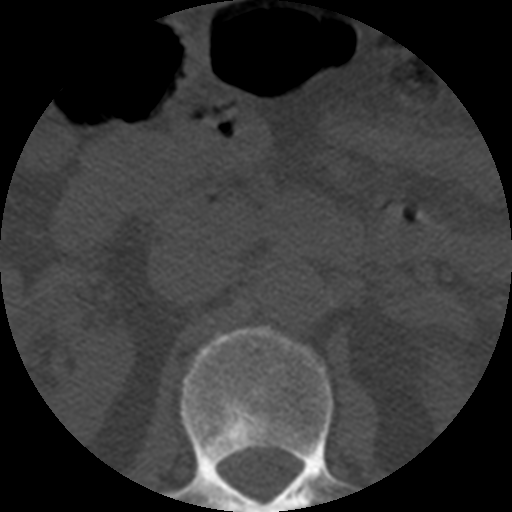
CT including the spine, one axial slice; slice 180 of 508 in the series (ordered by position); 120 kVp; bone window (W 1800 / L 400 HU); 1.25 mm slice thickness; 512 × 512 image matrix. Patient age 57 years. Case-level facts recorded for this patient, not image findings: primary cancer: prostate.
Structures marked on this image (semi-automatically segmented with operator editing):
- L1 vertebra: bounding box <169,328,357,512> (left, top, right, bottom; pixels)